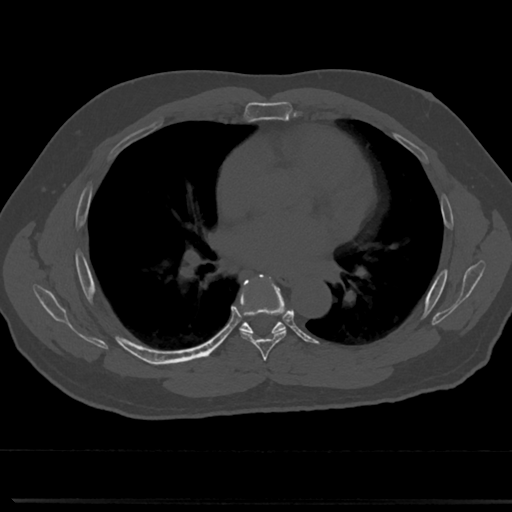
CT including the spine, one axial slice. Position 435 of 817 along the scan axis. Bone window (W 1800 / L 400 HU). 0.5 mm slice thickness. 512 × 512 image matrix, field of view 355 × 355 mm. Patient: male, 61 years. Case-level facts recorded for this patient, not image findings: primary cancer: prostate.
Annotated regions visible in this slice (semi-automatically segmented with operator editing):
- T5 vertebra: bounding box <265,369,272,377> (left, top, right, bottom; pixels)
- T6 vertebra: <237,277,303,354>
- T7 vertebra: <243,328,280,333>